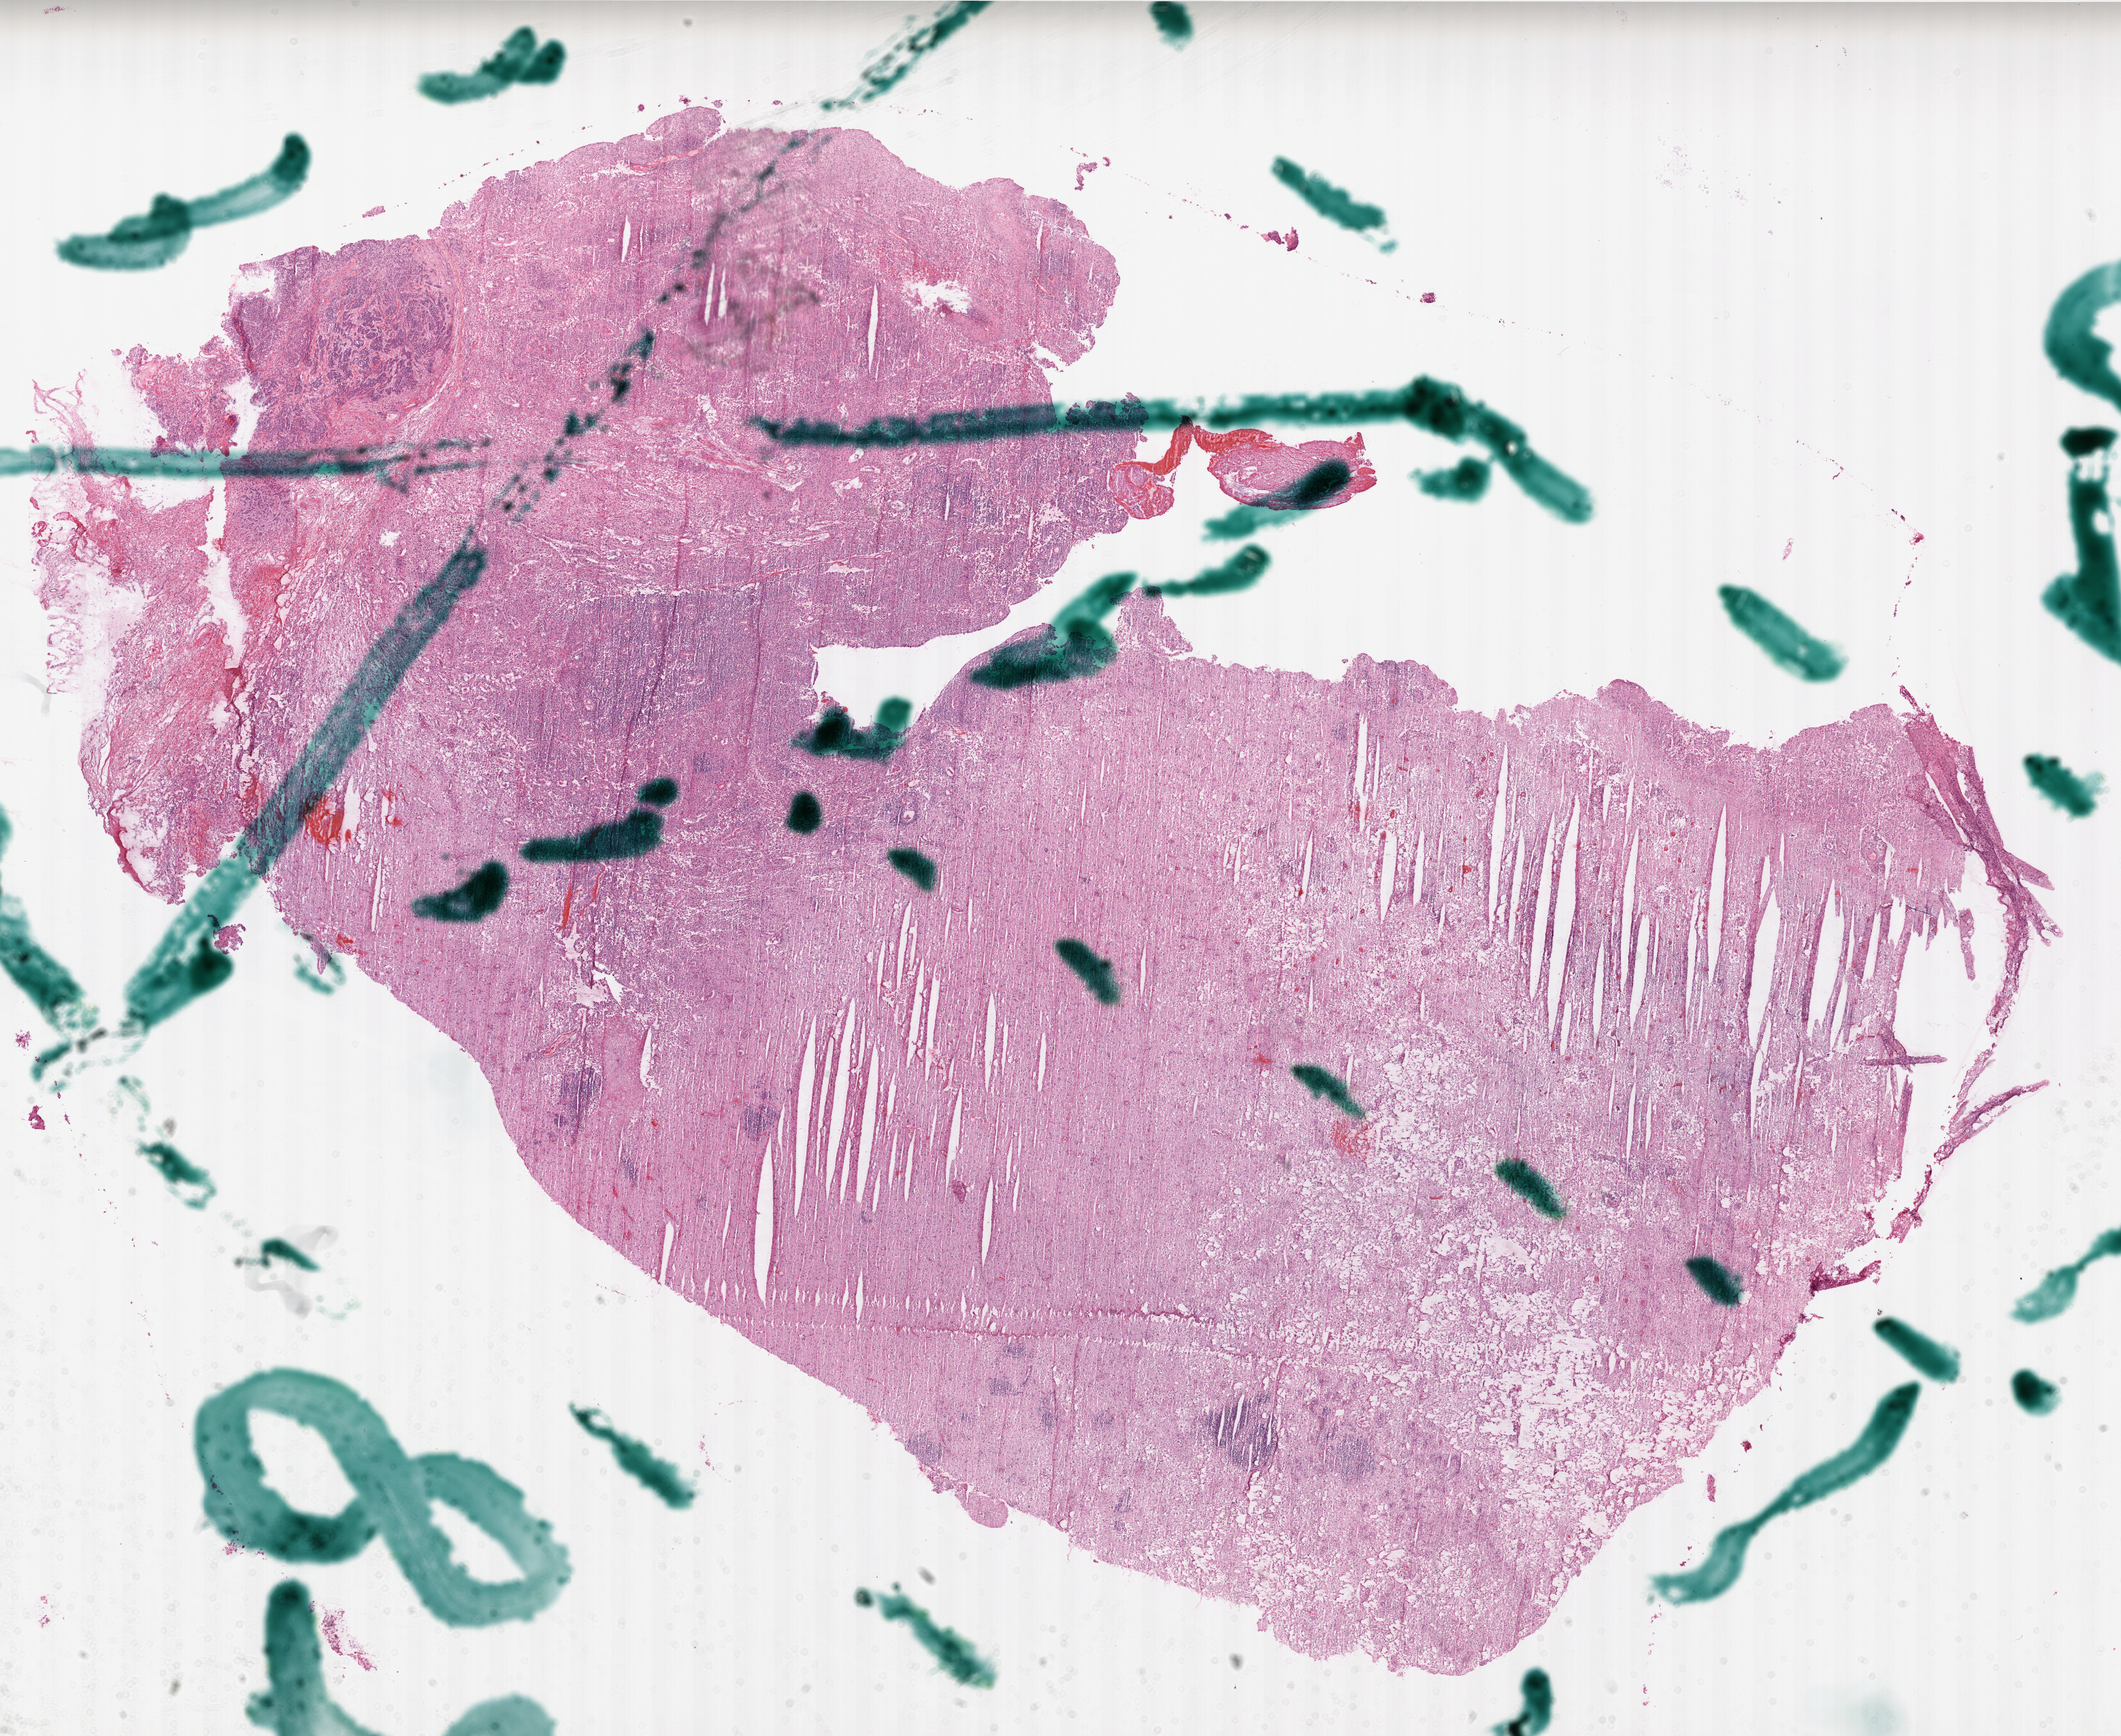
H&E whole-slide image, shown as a low-resolution overview of the whole scanned area (about 25.1 x 20.5 mm); frozen section from the top of the tissue portion; brain, primary tumour sample. Patient: male, age at initial diagnosis 46 years. Composition of this section per pathologist review: tumour cells 90%, tumour nuclei 100%, normal cells 0%, stromal cells 0%, necrosis 10%.
Diagnosis: Glioblastoma.